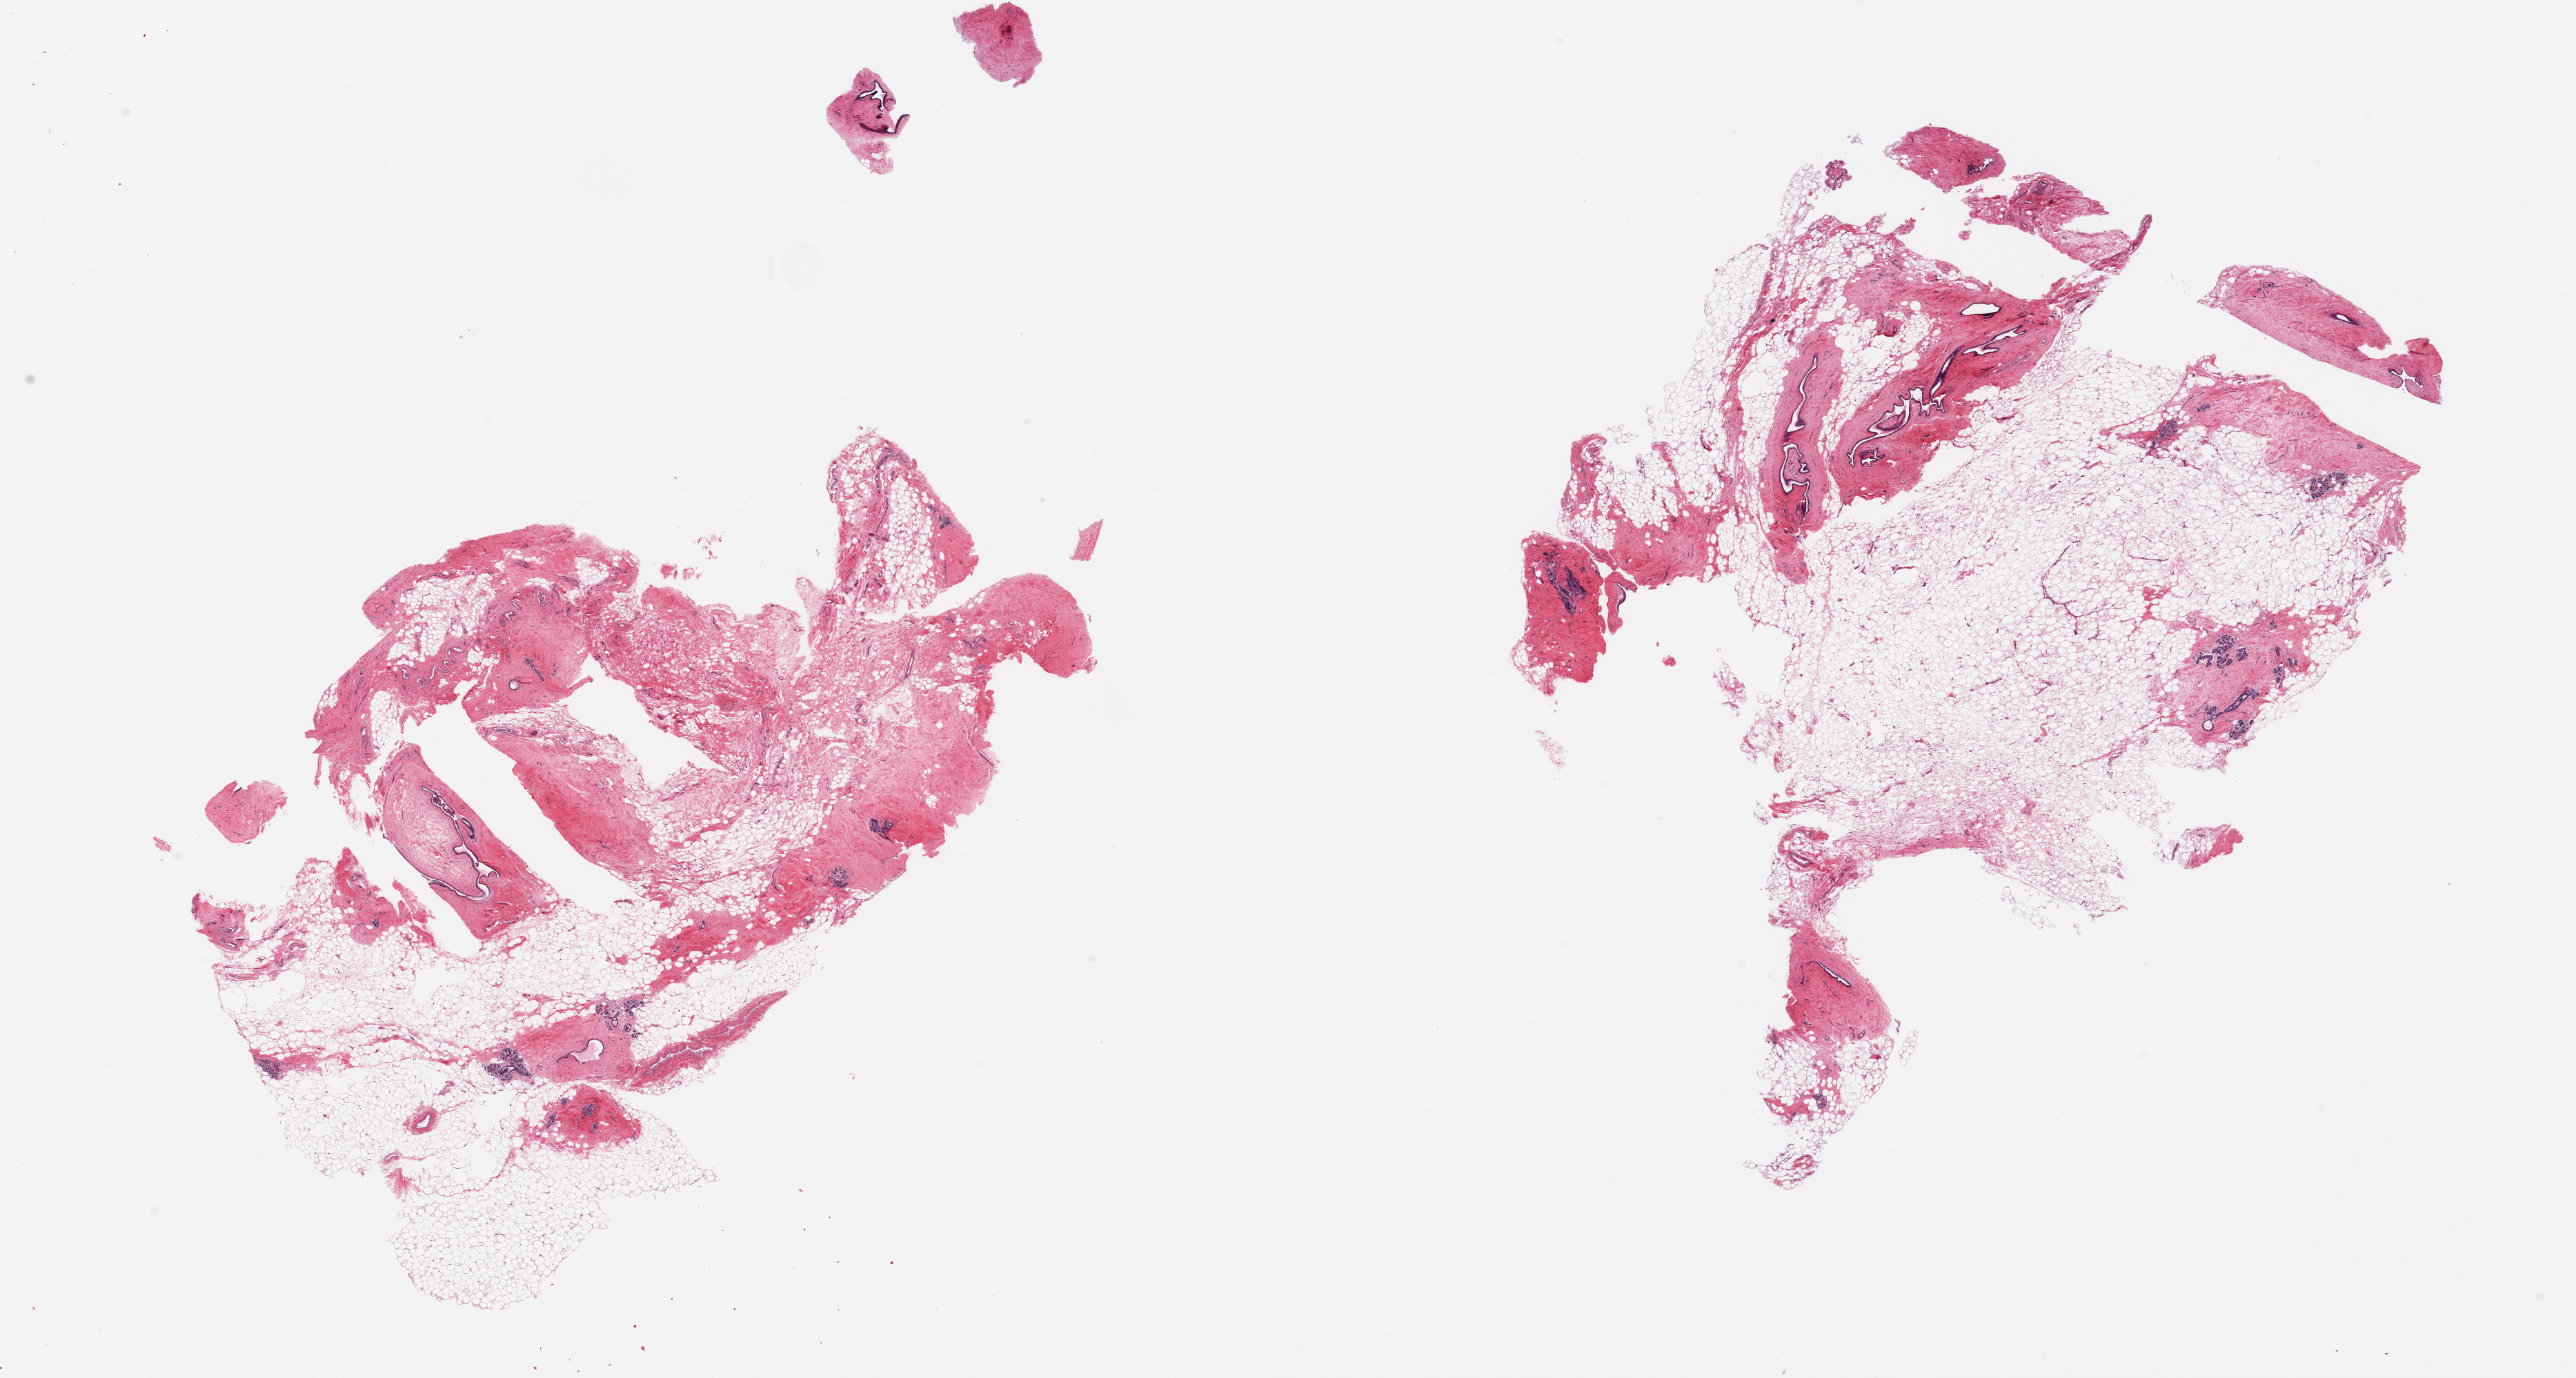
H&E whole-slide image, brightfield, shown as a low-resolution overview of the whole scanned area (about 29.5 x 15.8 mm). PAXgene-fixed, paraffin-embedded tissue. Section of breast (target tissue). Donor tissue sample. Female donor.
Review note (as recorded): 2 pieces, fibrous mastopathy; ductal/lobular elements atrophic.